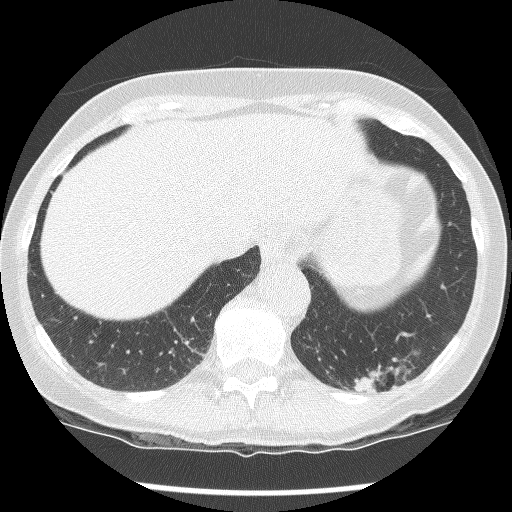
Low-dose screening chest CT, axial slice, second annual screen, lung window (W 1500 / L -600 HU), lung (sharp) reconstruction kernel (BONE), 512 × 512 image matrix, field of view 300 × 300 mm. Female, age 61 years at enrolment. Current smoker at enrolment.
Expert reader's lesion annotation, bounding box <327,309,440,412> (left, top, right, bottom; pixels). The screening reader recorded 2 non-calcified nodules or masses ≥4 mm on this exam (left lower lobe, left lower lobe); which of them this box marks is not recorded. Official screen result: positive, no significant change: stable abnormalities potentially related to lung cancer, unchanged since the prior screening exam. Lung cancer was diagnosed 585 days after this screen (after the third annual screen): non-small cell carcinoma, left lower lobe, poorly differentiated (G3), stage IB (AJCC 6th edition), 100 mm at pathology.